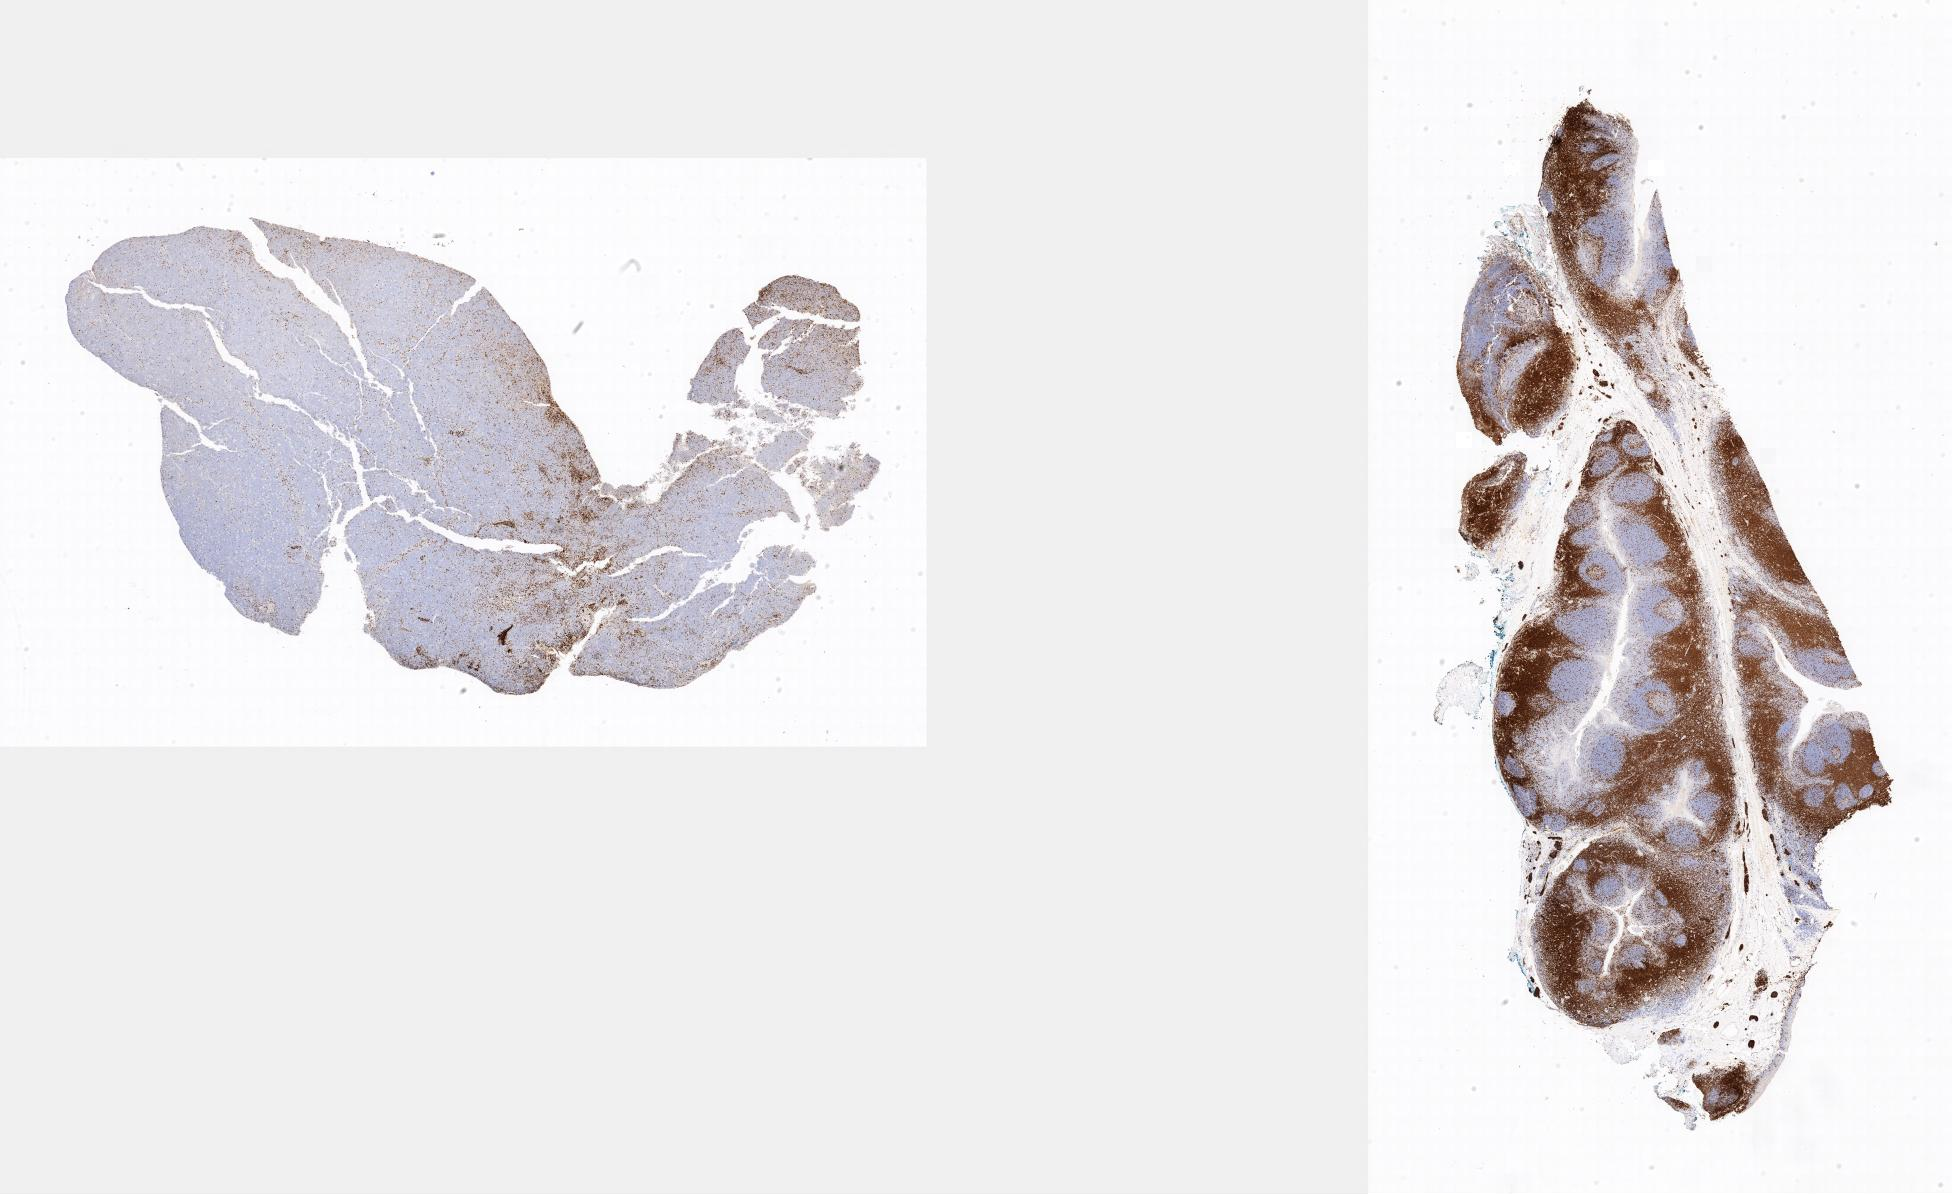
Whole-slide image, immunohistochemical stain for CD3 — whole scanned area shown as a low-resolution overview, specimen: tumor tissue, anatomic site: lymph node of head and neck. Male, age 5 years at initial diagnosis.
Diagnosis: Burkitt lymphoma, NOS.